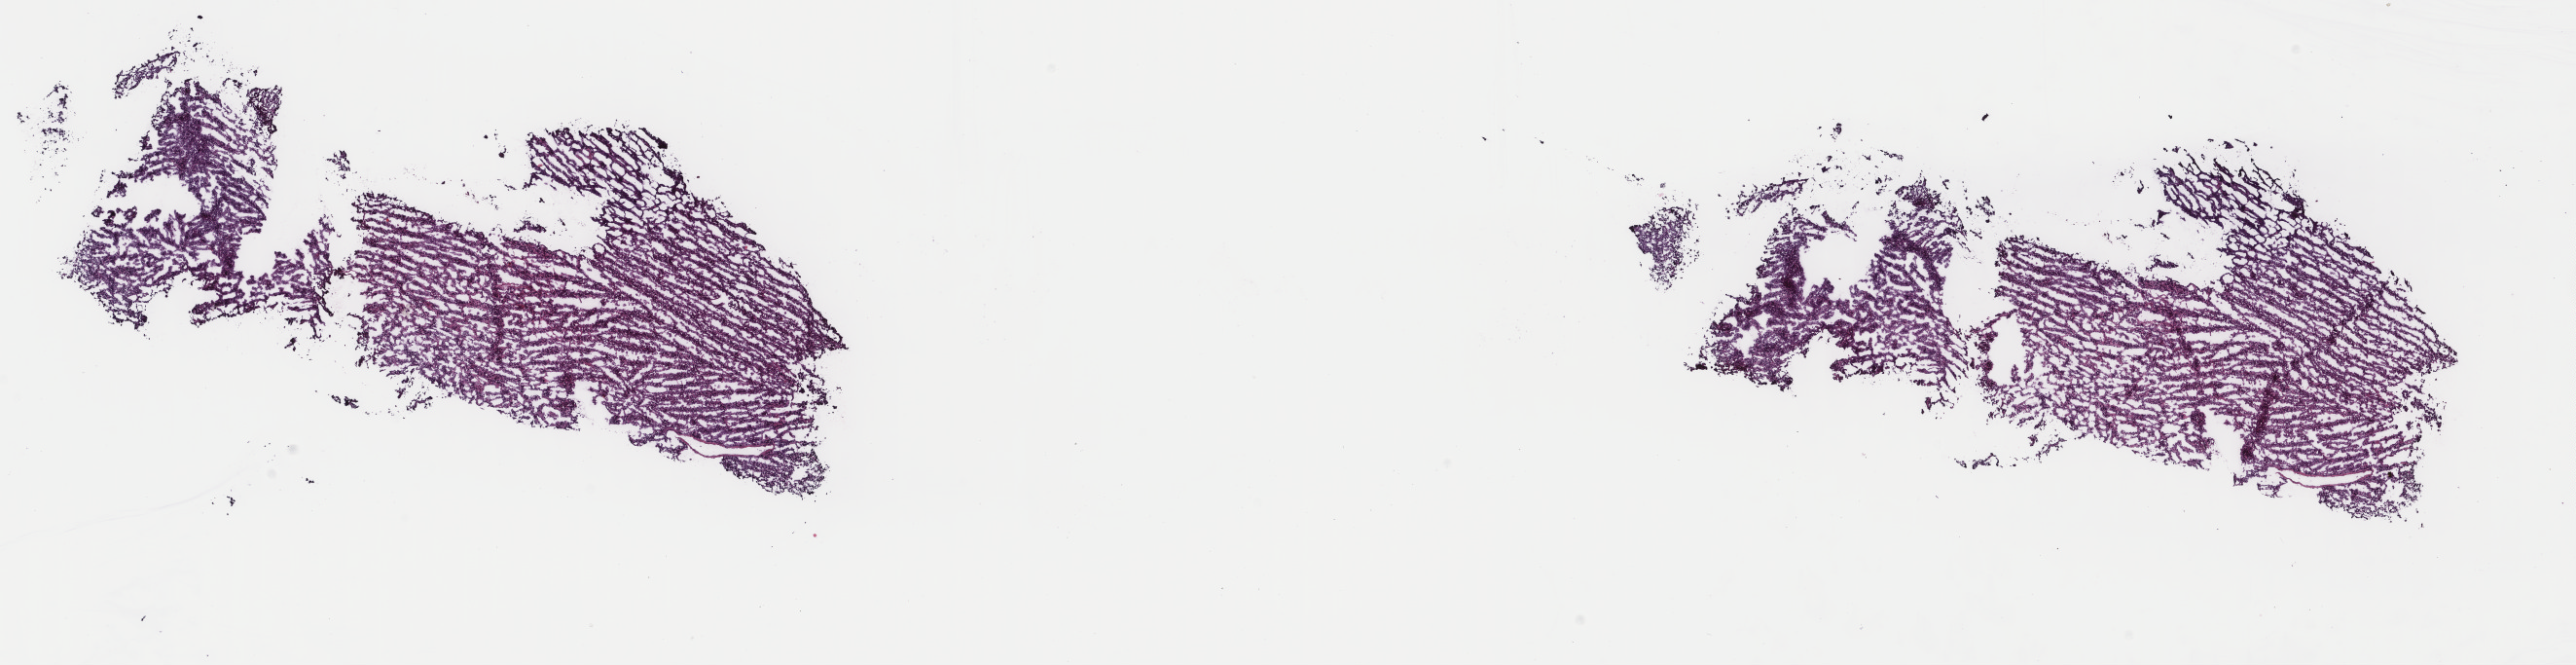
Digitized H&E-stained tissue section (whole slide), whole scanned area (about 21.0 x 5.4 mm) shown as a low-resolution overview. Frozen section. Sample: primary tumour, adrenal cortex. Male patient; age at initial diagnosis 58 years. Pathologist review of this section (percent, as recorded): tumour cells 100%, tumour nuclei 80%, normal cells 0%, stromal cells 0%, necrosis 0%. Inflammatory infiltration, as recorded: lymphocyte infiltration 2%, monocyte infiltration 0%, neutrophil infiltration 0%.
• histologic diagnosis: Adrenal cortical carcinoma (cortex of adrenal gland)